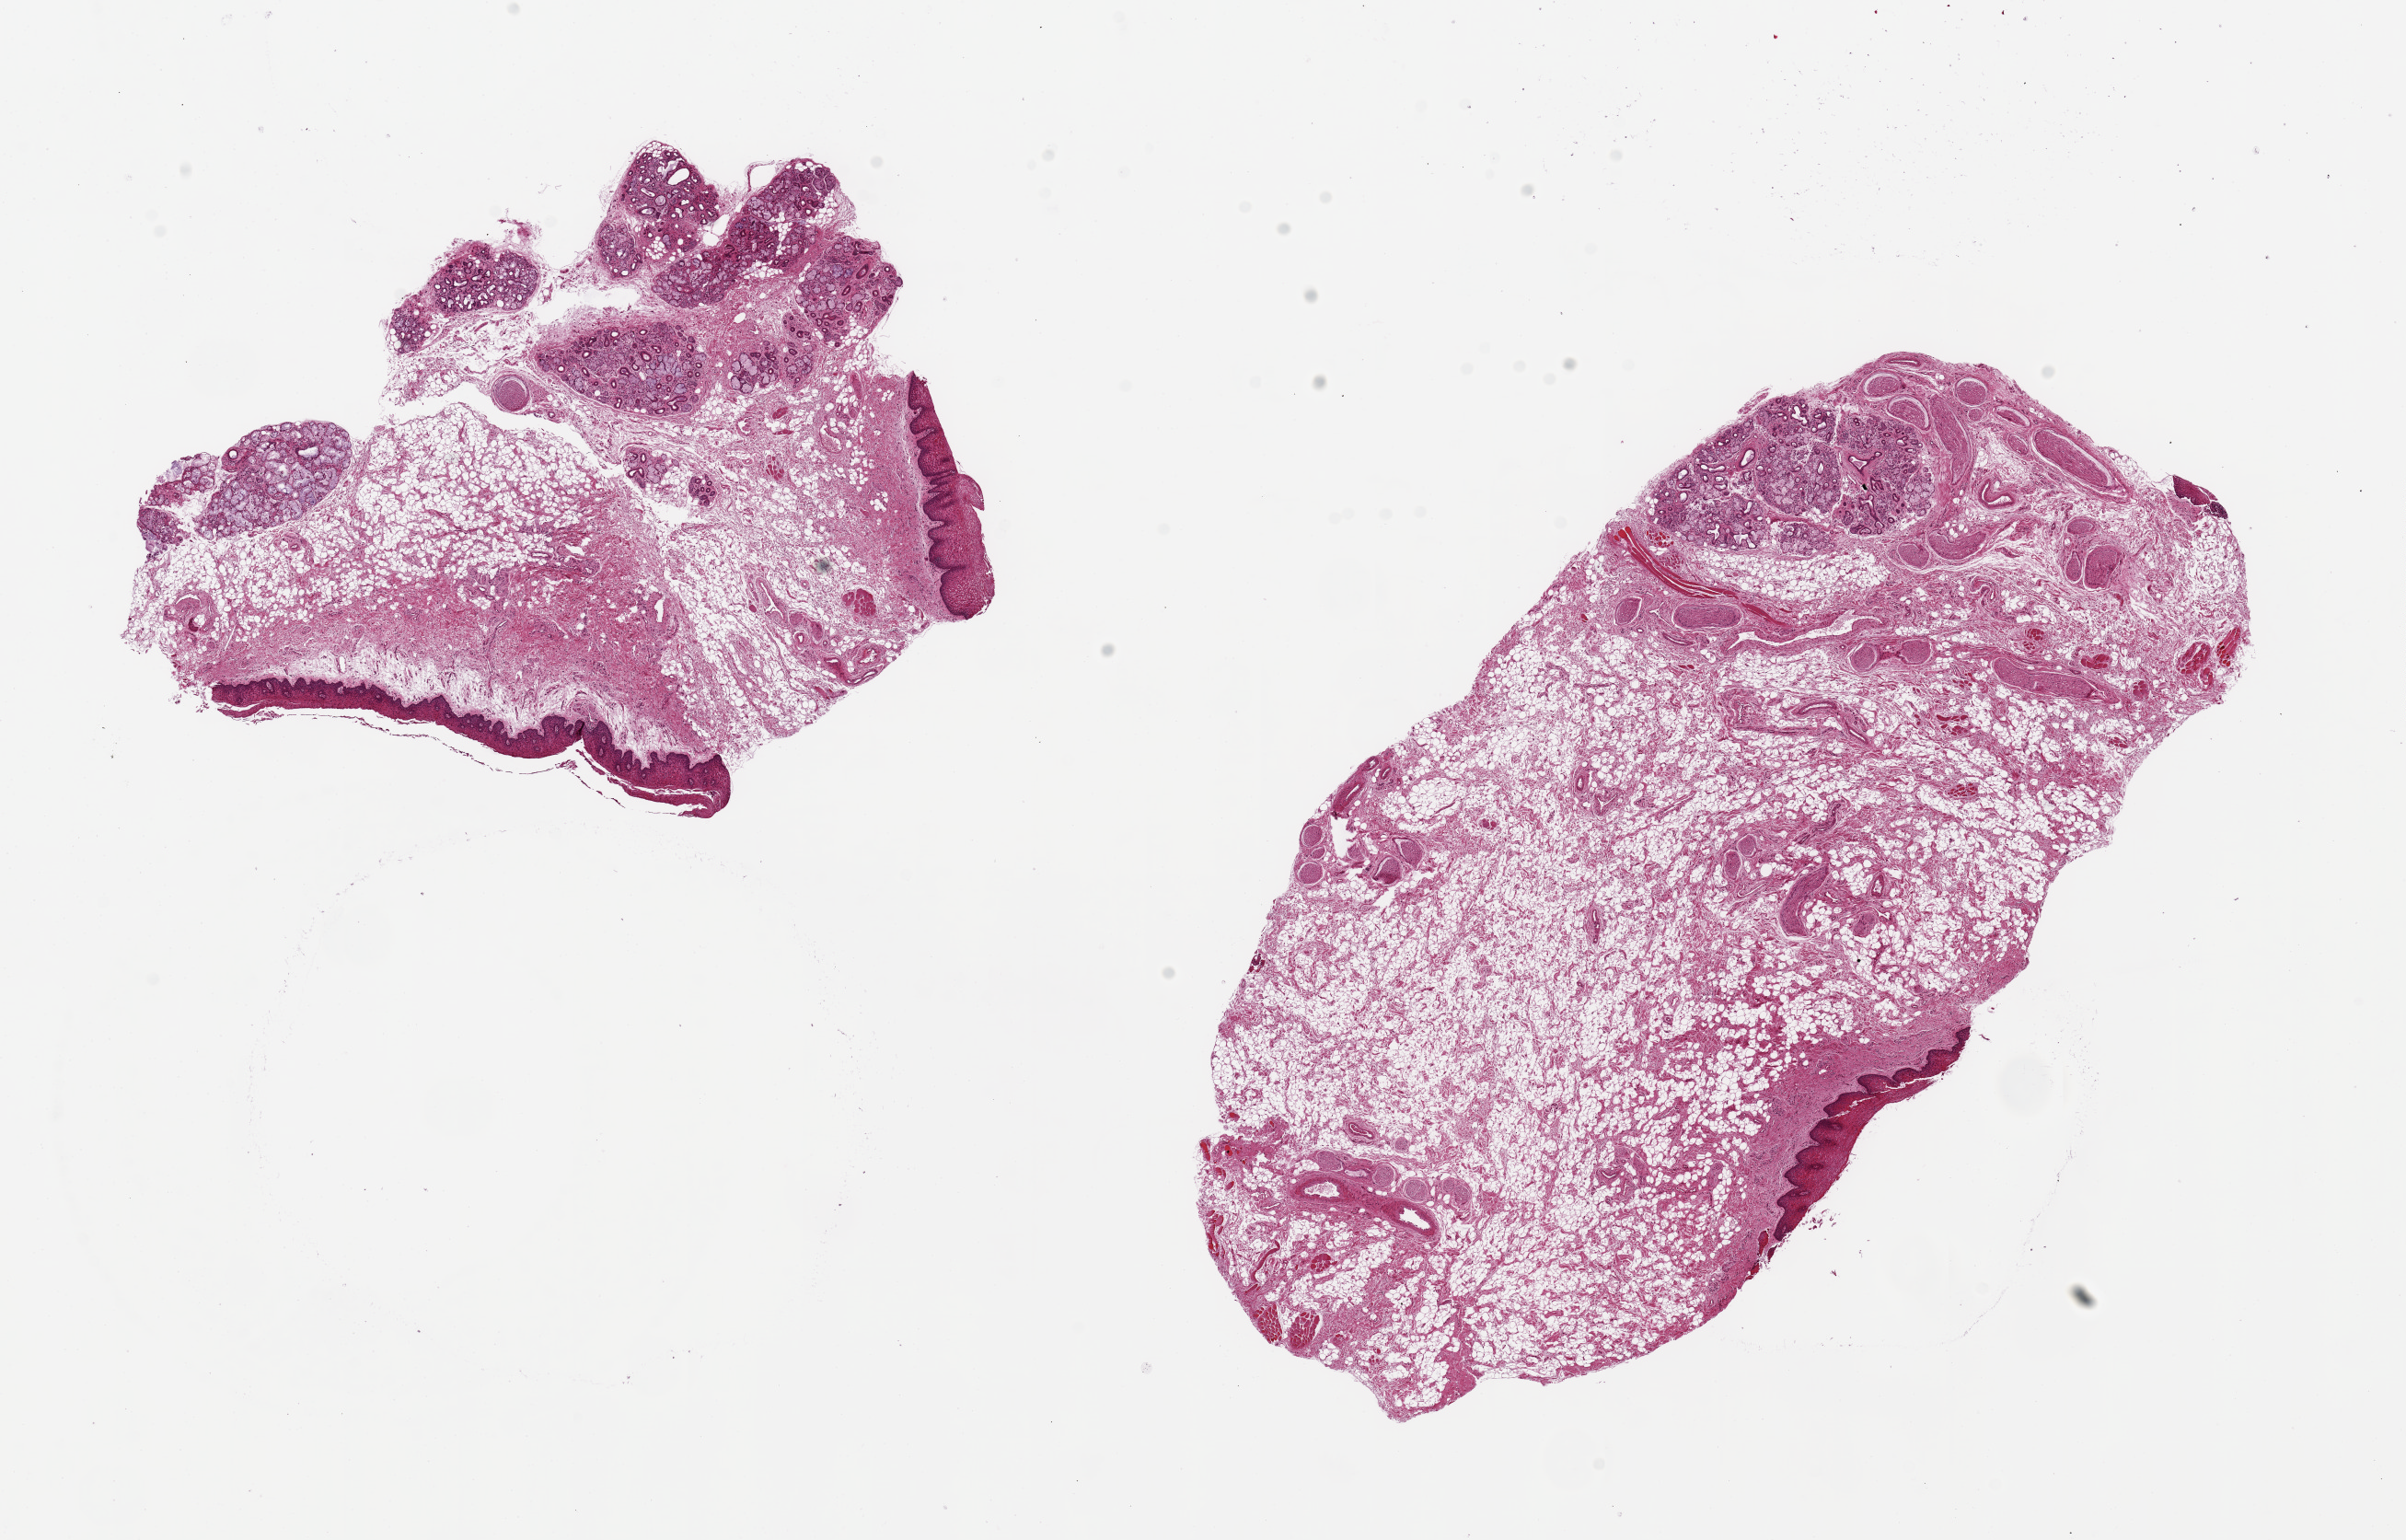
Whole-slide image, hematoxylin and eosin (H&E) stain — low-resolution overview of the scanned area, about 20.7 x 13.2 mm. PAXgene-fixed paraffin-embedded (PFPE) section. Sampled site (target tissue): minor salivary gland. Tissue donor sample. Female donor.
Pathologist's review note for this sample: 2 pieces, 7x5.5 & 11x6mm; <10% glands, mainly mucosa and submucosal stroma/fat.